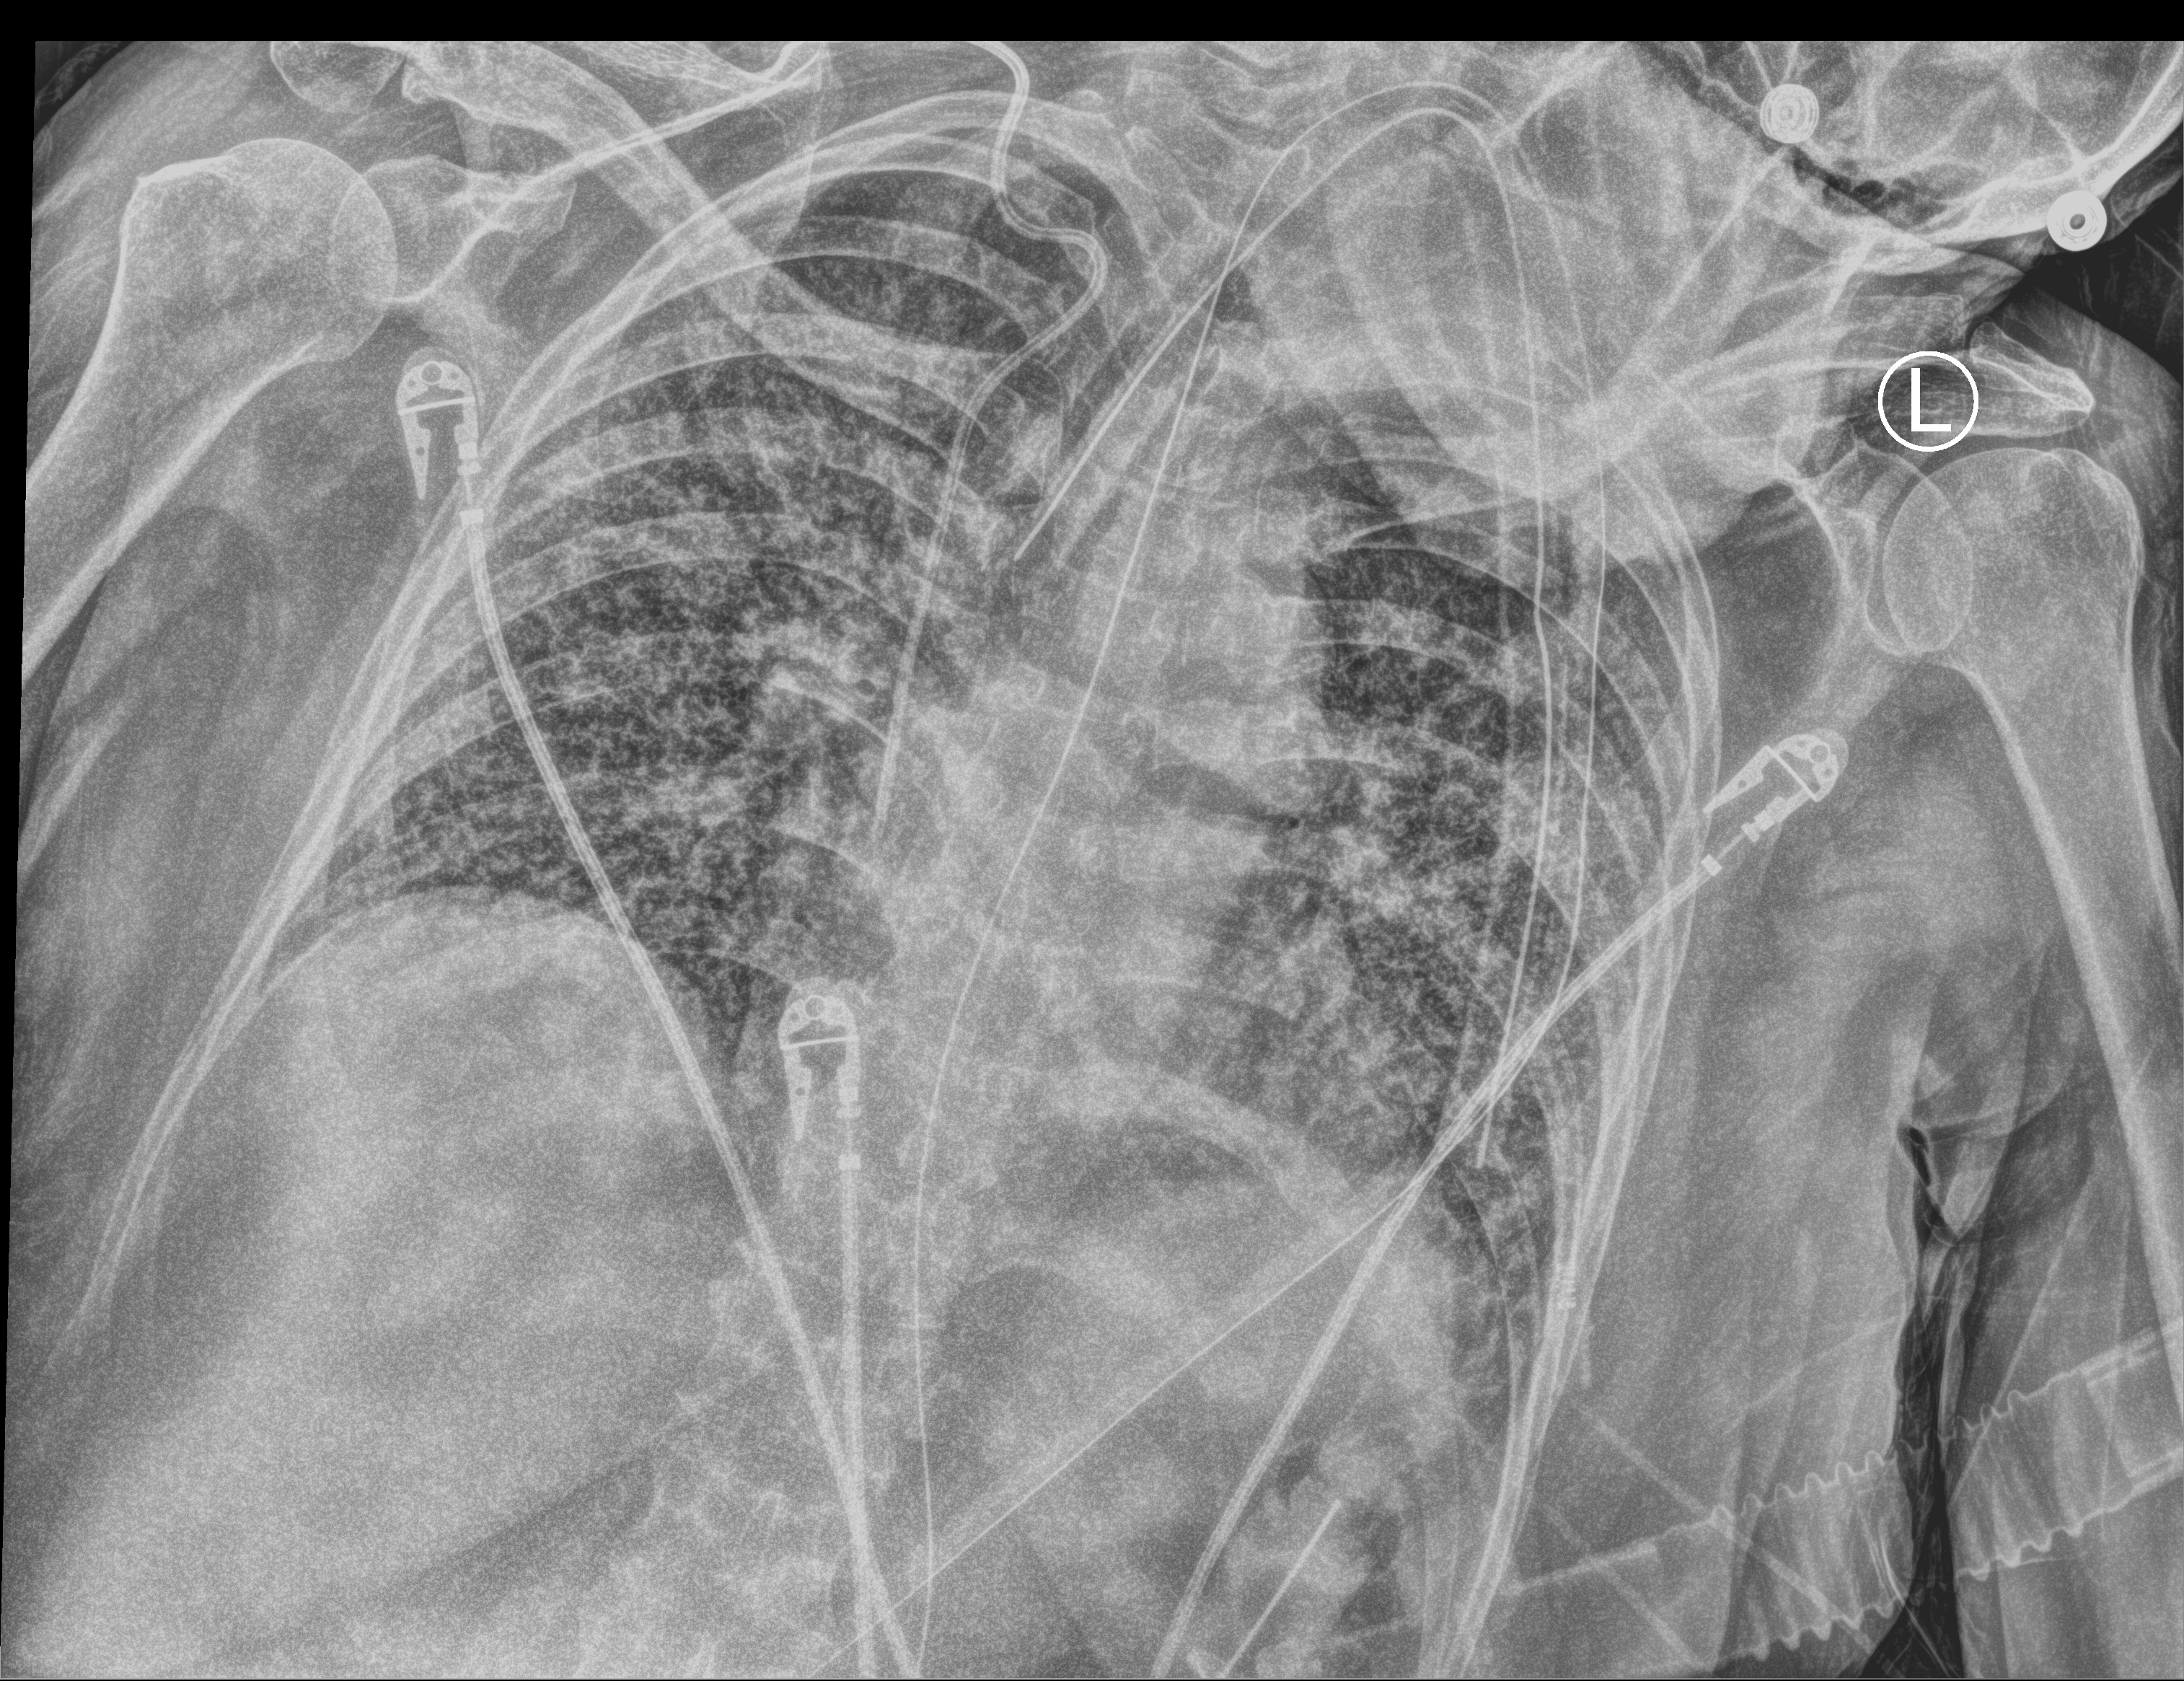
Bedside chest radiograph (computed radiography), anteroposterior (AP) projection. Patient hospitalised with COVID-19; female, aged 60–74 years.
Hospital-stay facts (about this admission, not read from this image; timing relative to this image not recorded):
- admitted to intensive care during this hospital stay: yes
- COPD (admission record): no